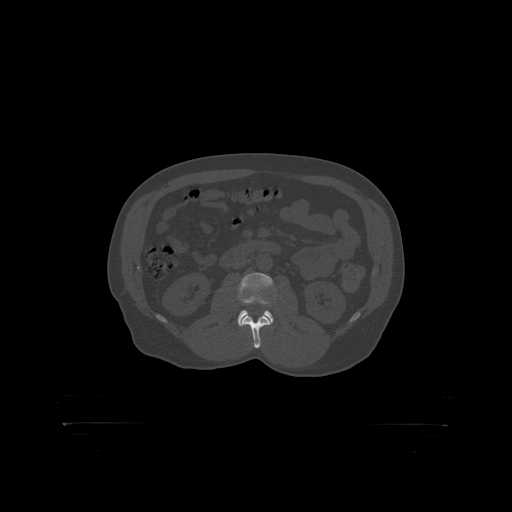
CT including the spine, one axial slice. Slice 282 of 399 in the series (ordered by position). Bone window (W 1800 / L 400 HU). 1.25 mm slice thickness. 512 × 512 image matrix. Patient: male, 46 years. Case-level facts recorded for this patient, not image findings: primary cancer: skin.
Structures marked on this image (semi-automatic segmentation, software-assisted and operator-edited):
- L2 vertebra: box from (x=243, y=315) to (x=267, y=319) px
- L3 vertebra: (x=238, y=273)–(x=274, y=318)